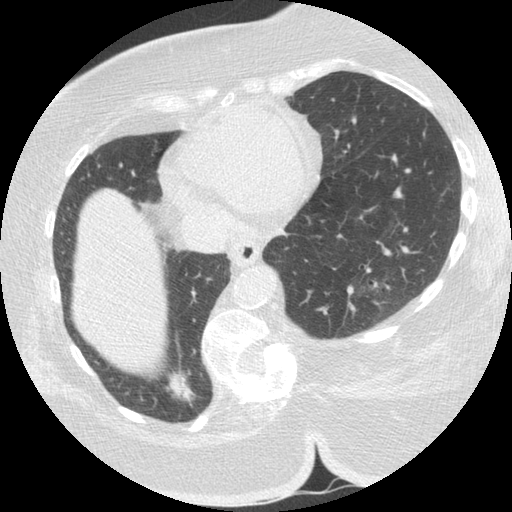
Low-dose screening chest CT, one axial slice. Position 50 of 151 along the scan axis. Lung window (W 1500 / L -600 HU). 2.5 mm slice thickness. 512 × 512 image matrix, field of view 340 × 340 mm.
Structures marked on this image (outlined manually by an expert reader):
- lesion 1 (tumor, lower lobe of right lung): bounding box (x1, y1, x2, y2) in pixels: (165, 370, 196, 406)